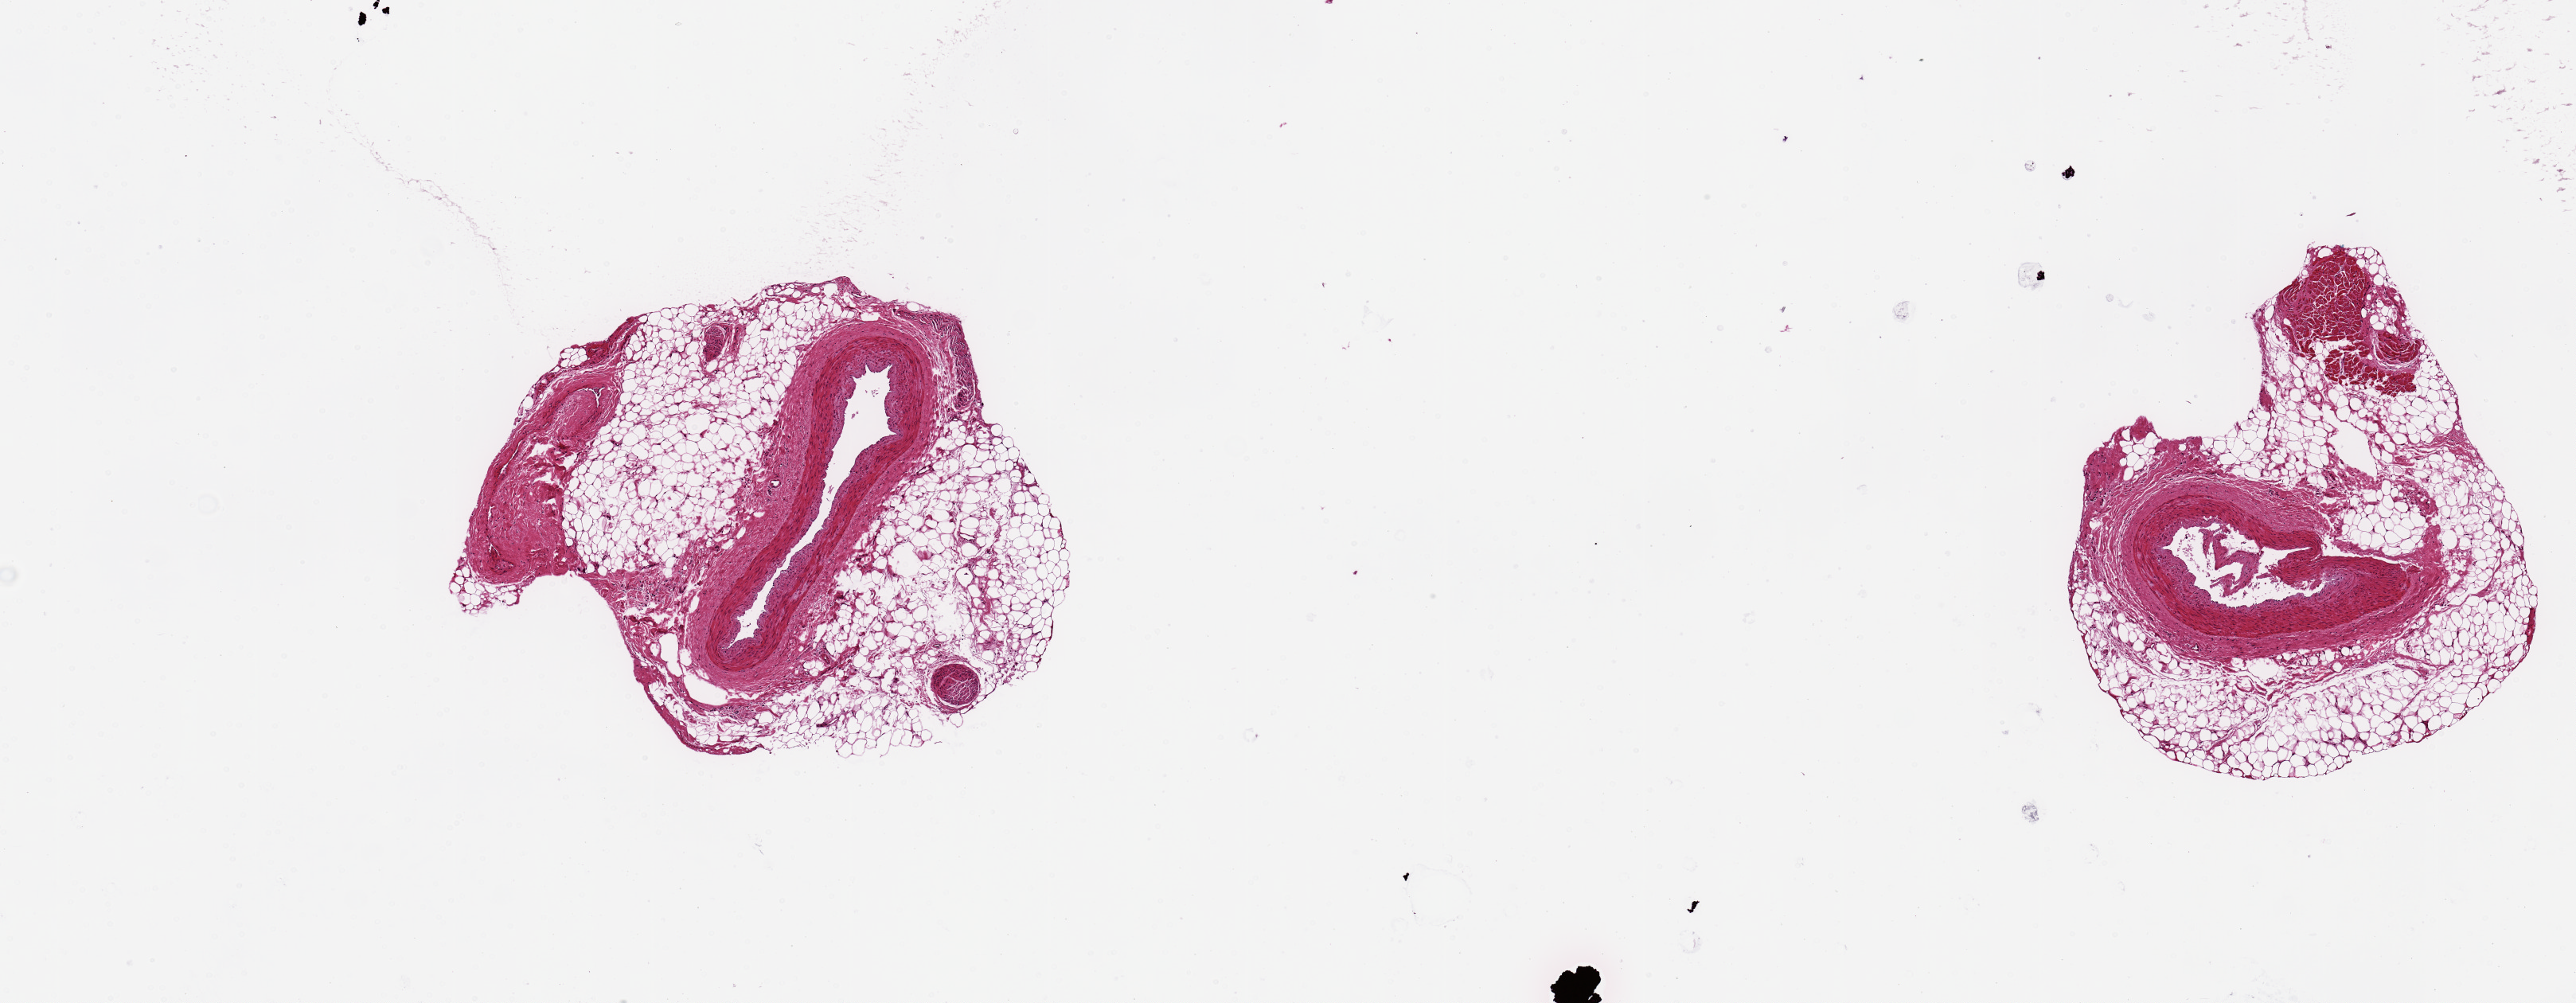
Whole-slide image, H&E stain, whole scanned area (about 12.8 x 5.0 mm, acquisition: 20x scan) shown as a low-resolution overview, PAXgene-fixed, paraffin-embedded tissue, sampled site (target tissue): coronary artery, tissue donor sample.
Review note (as recorded): artery is 20% of aliquot.